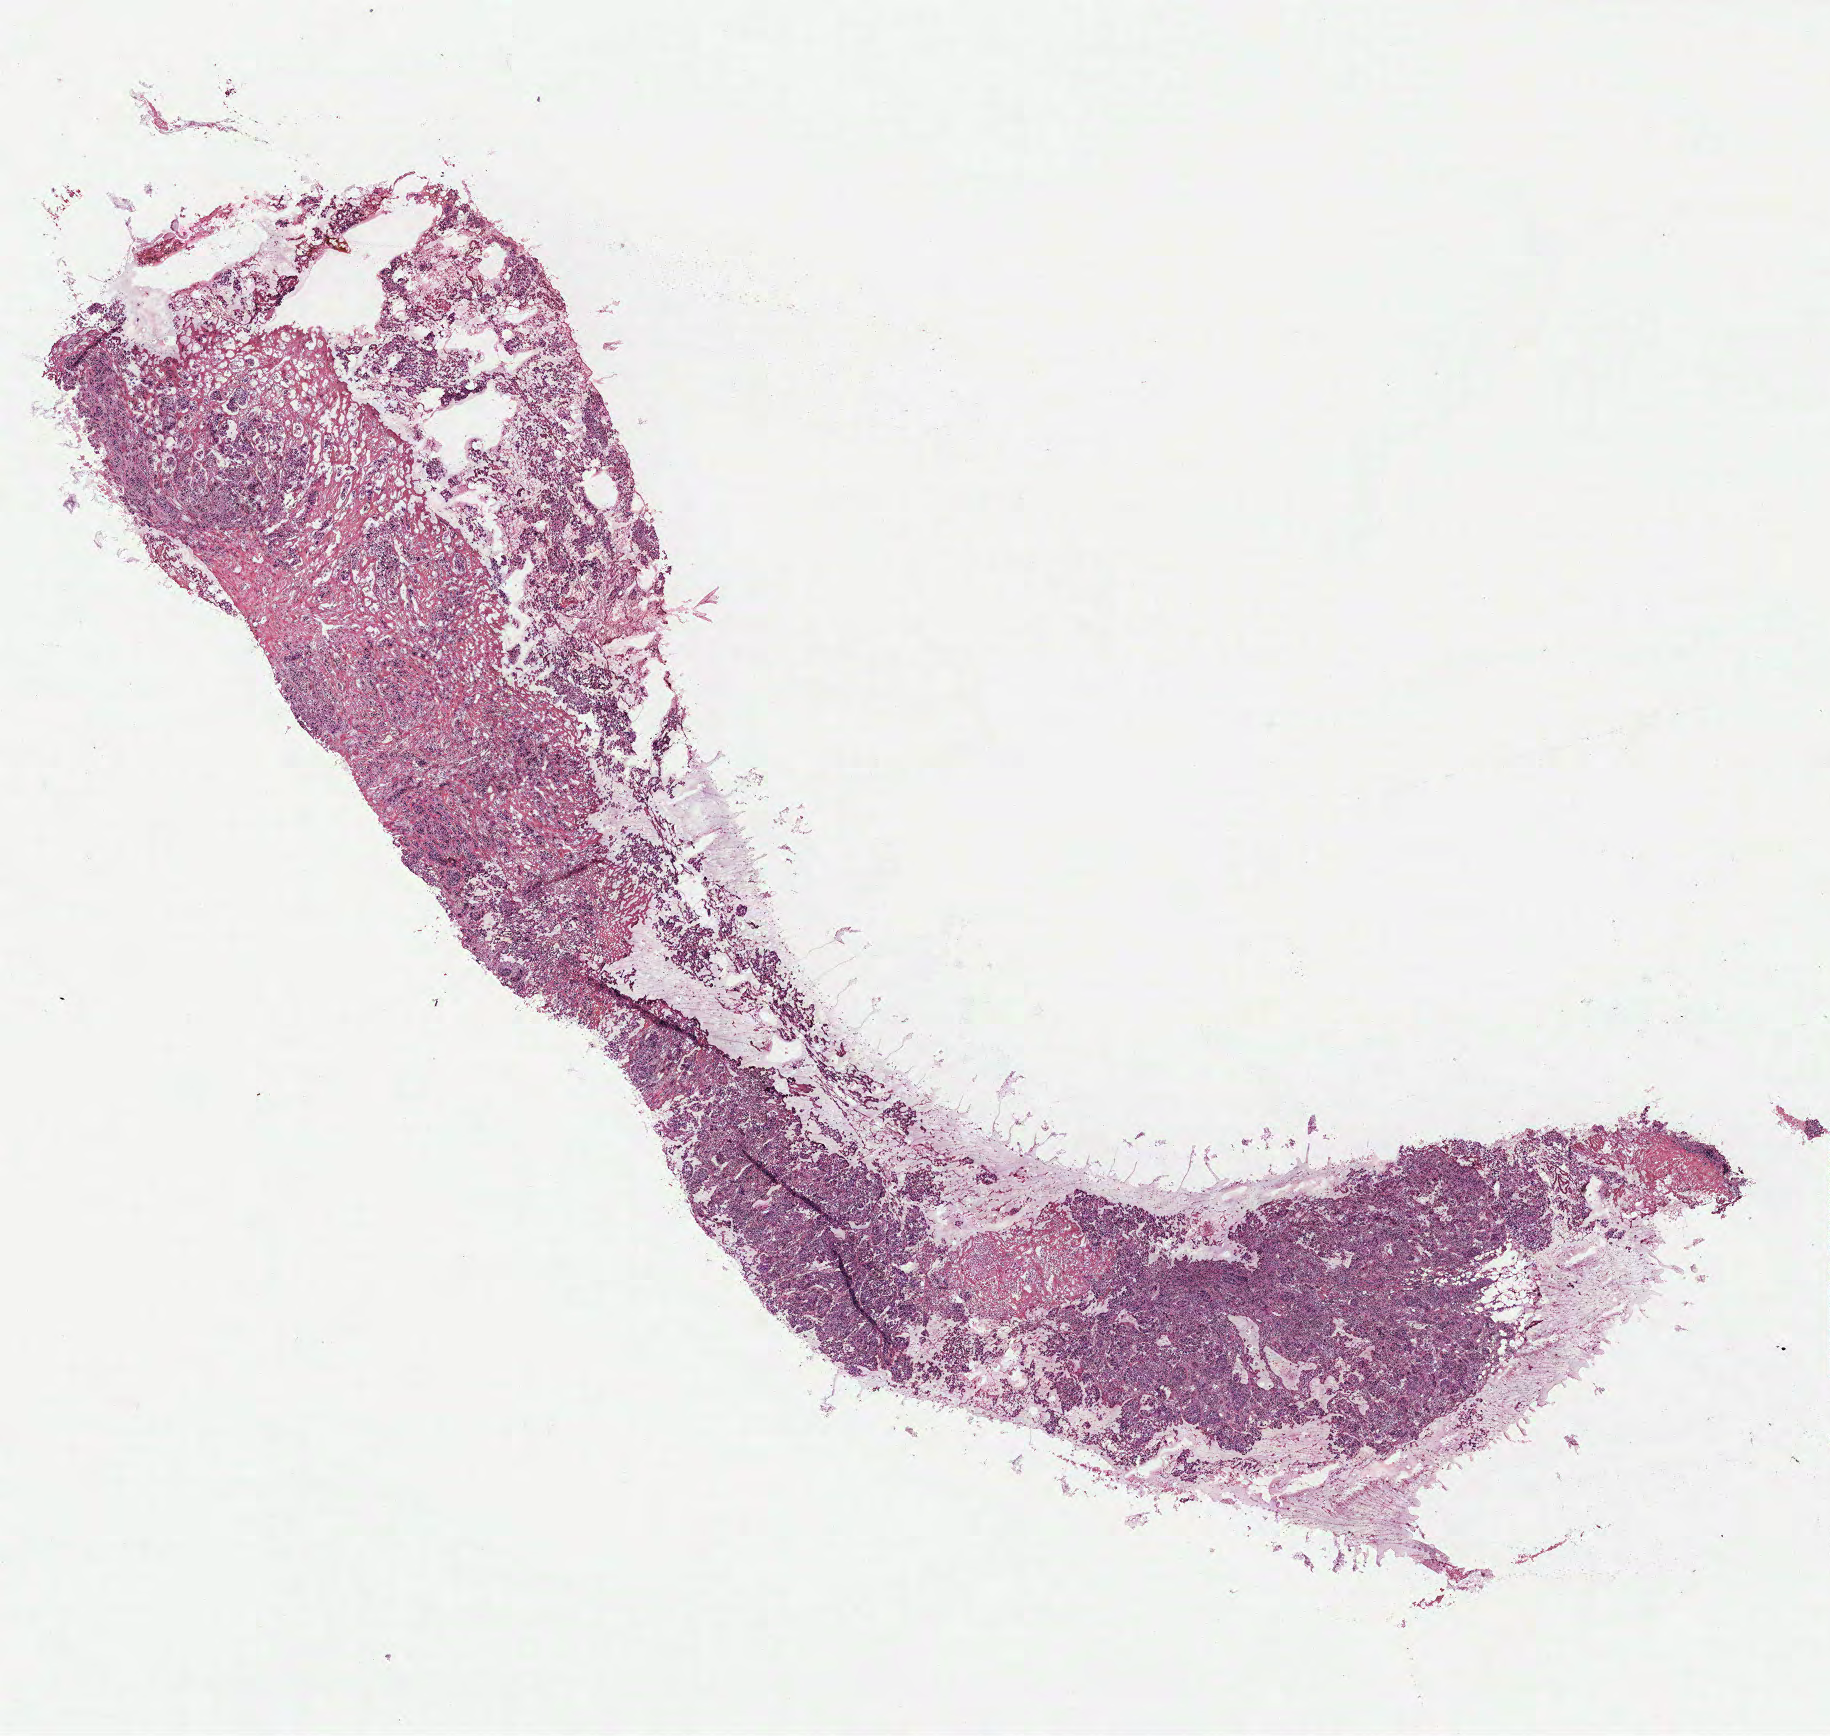
Whole-slide histology image, H&E-stained — low-resolution overview of the scanned area, about 14.6 x 13.9 mm (from a 40x scan). Breast, tumour tissue. 55-year-old female patient.
AJCC pathologic stage: IIB. Histologic diagnosis: Infiltrating duct carcinoma, NOS.